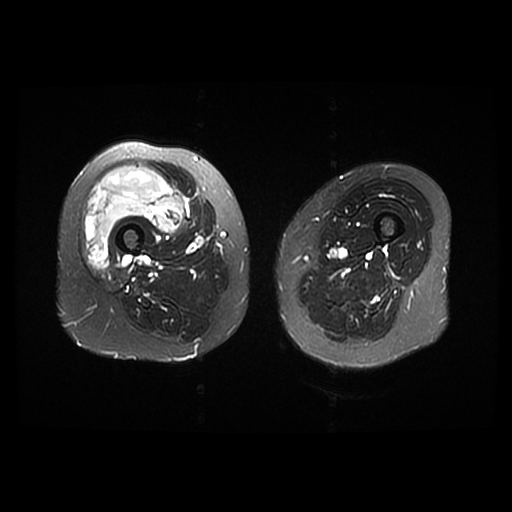
MRI of an extremity soft-tissue mass, one axial slice. Slice 15 of 42 in the series (ordered by position). T2-weighted fat-saturated. 512 × 512 image matrix. Female patient. From the clinical record (not read from this slice): histological type: pleiomorphic undifferentiated sarcoma; grade: high; site of the primary tumour: right quadricep.
Structures marked on this image (outlined manually by an expert reader):
- gross tumour volume including surrounding oedema: bounding box <84,166,184,269> (left, top, right, bottom; pixels)
- gross tumour volume (mass): <84,166,184,269>